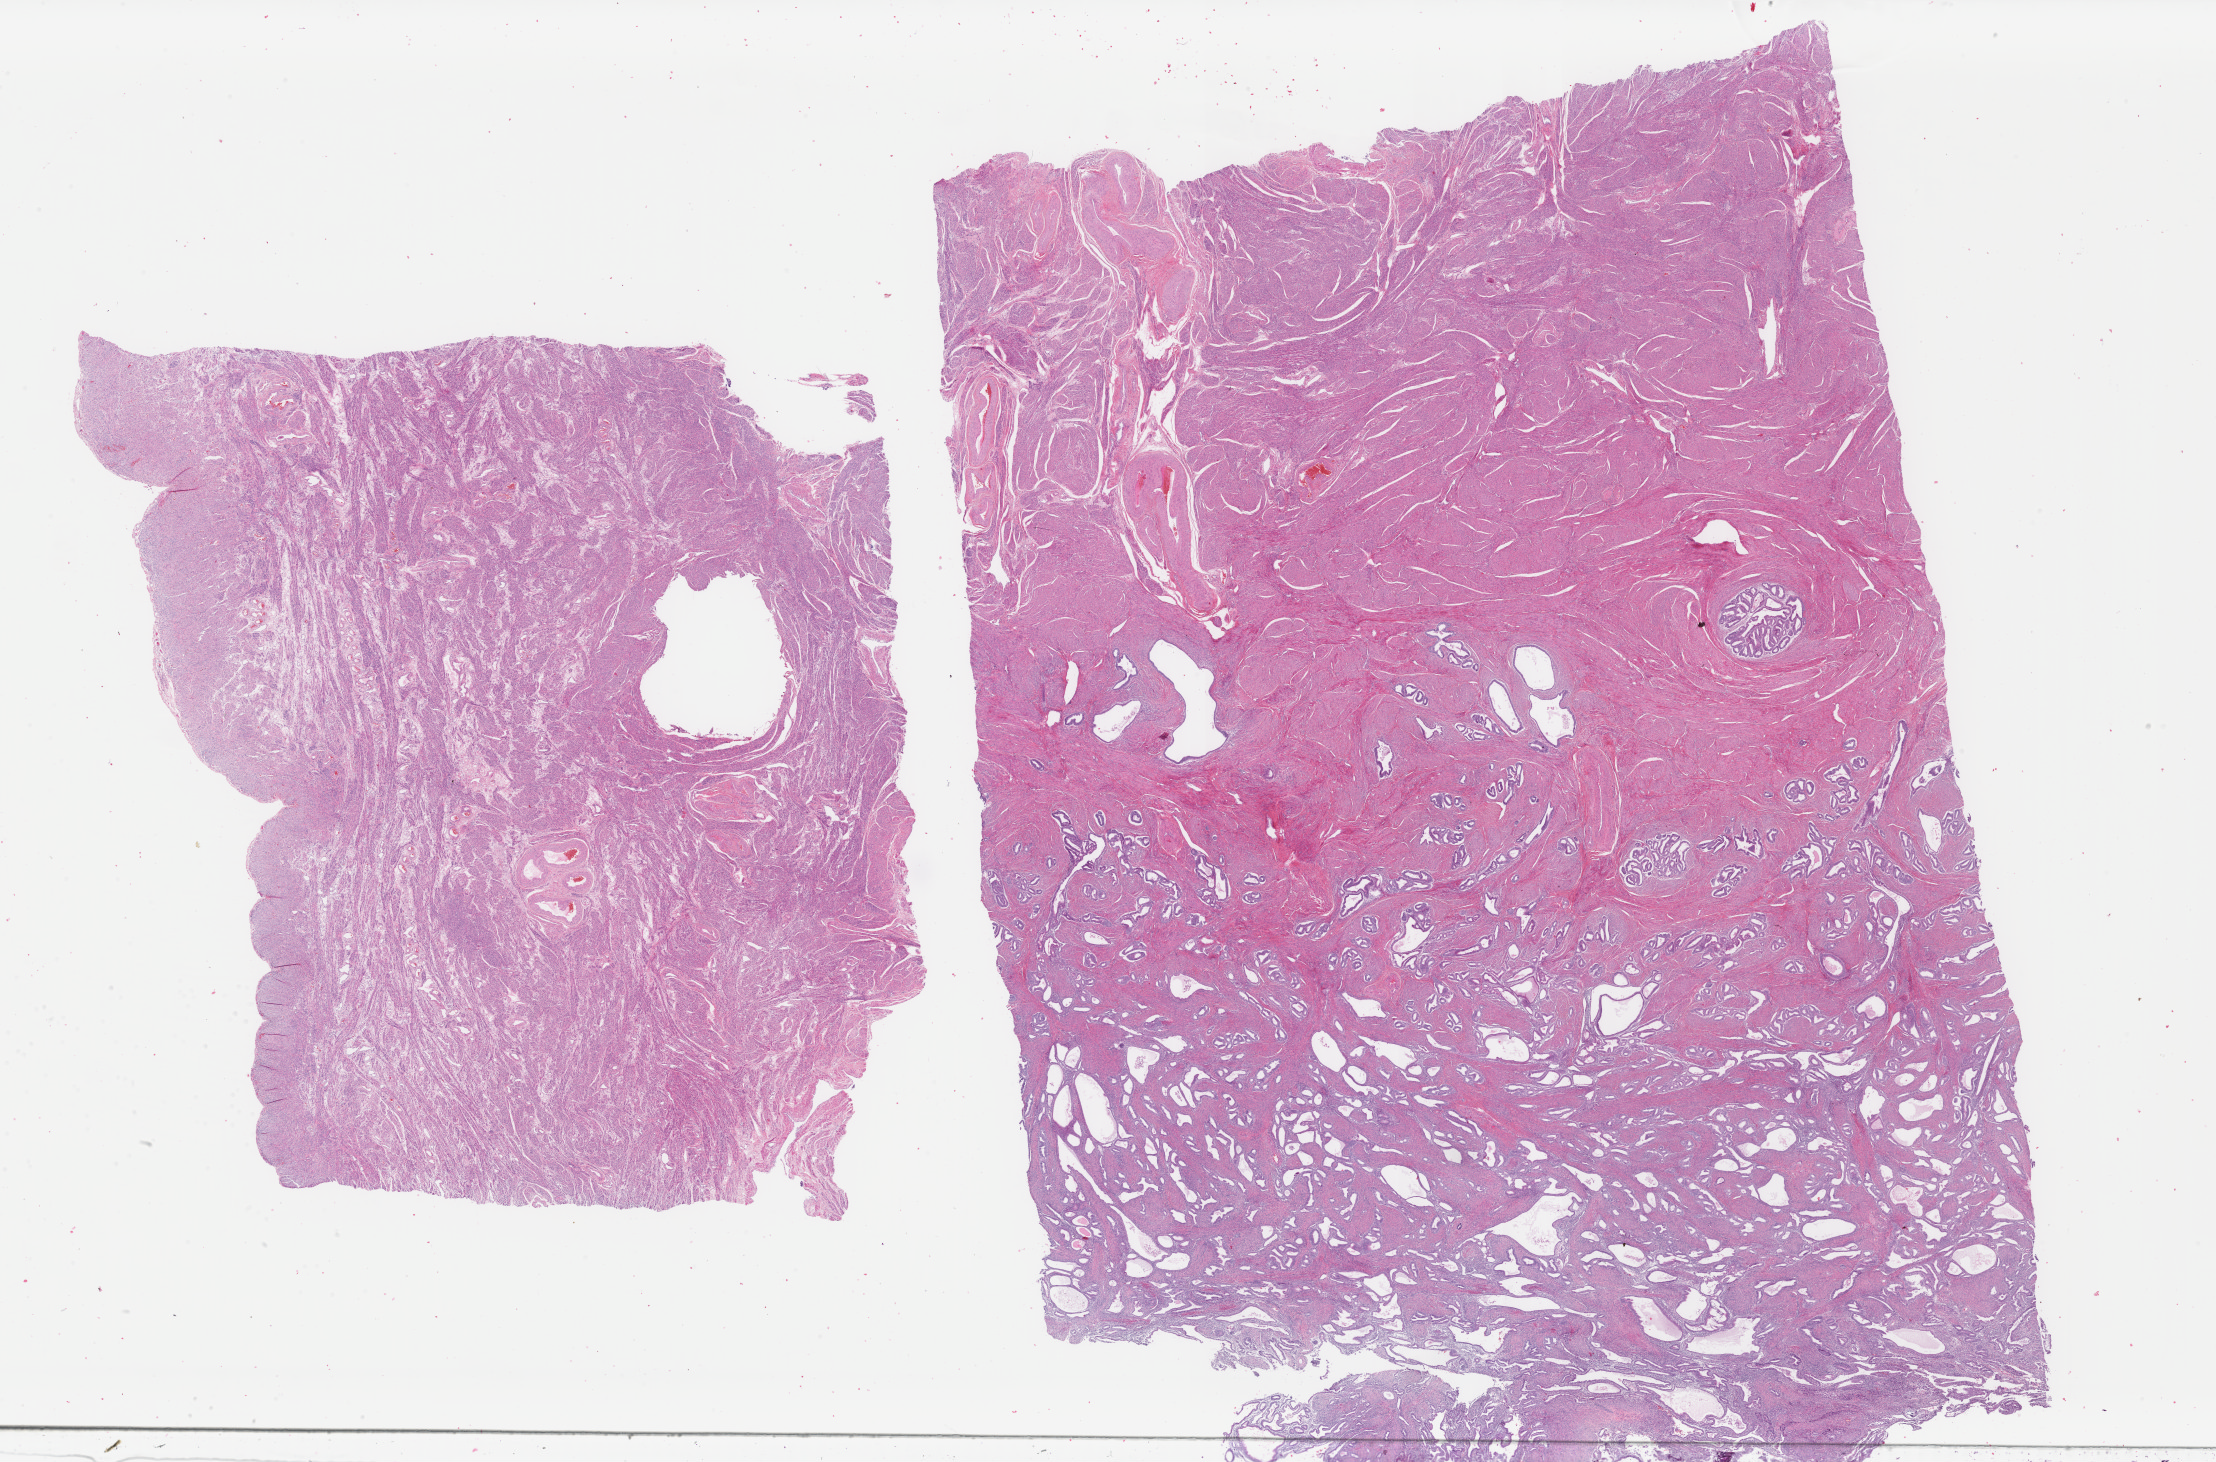
Digitized H&E tissue section (whole slide) — a low-resolution overview of the entire scanned area, about 35.2 x 23.2 mm (acquisition: 40x scan); formalin-fixed paraffin-embedded (FFPE) diagnostic section; primary tumour sample from the uterus. Patient: female, age at initial diagnosis 57 years. Histologic grade: G1 (well differentiated).
Pathologic diagnosis: Endometrioid adenocarcinoma, NOS. FIGO stage: IIIA.